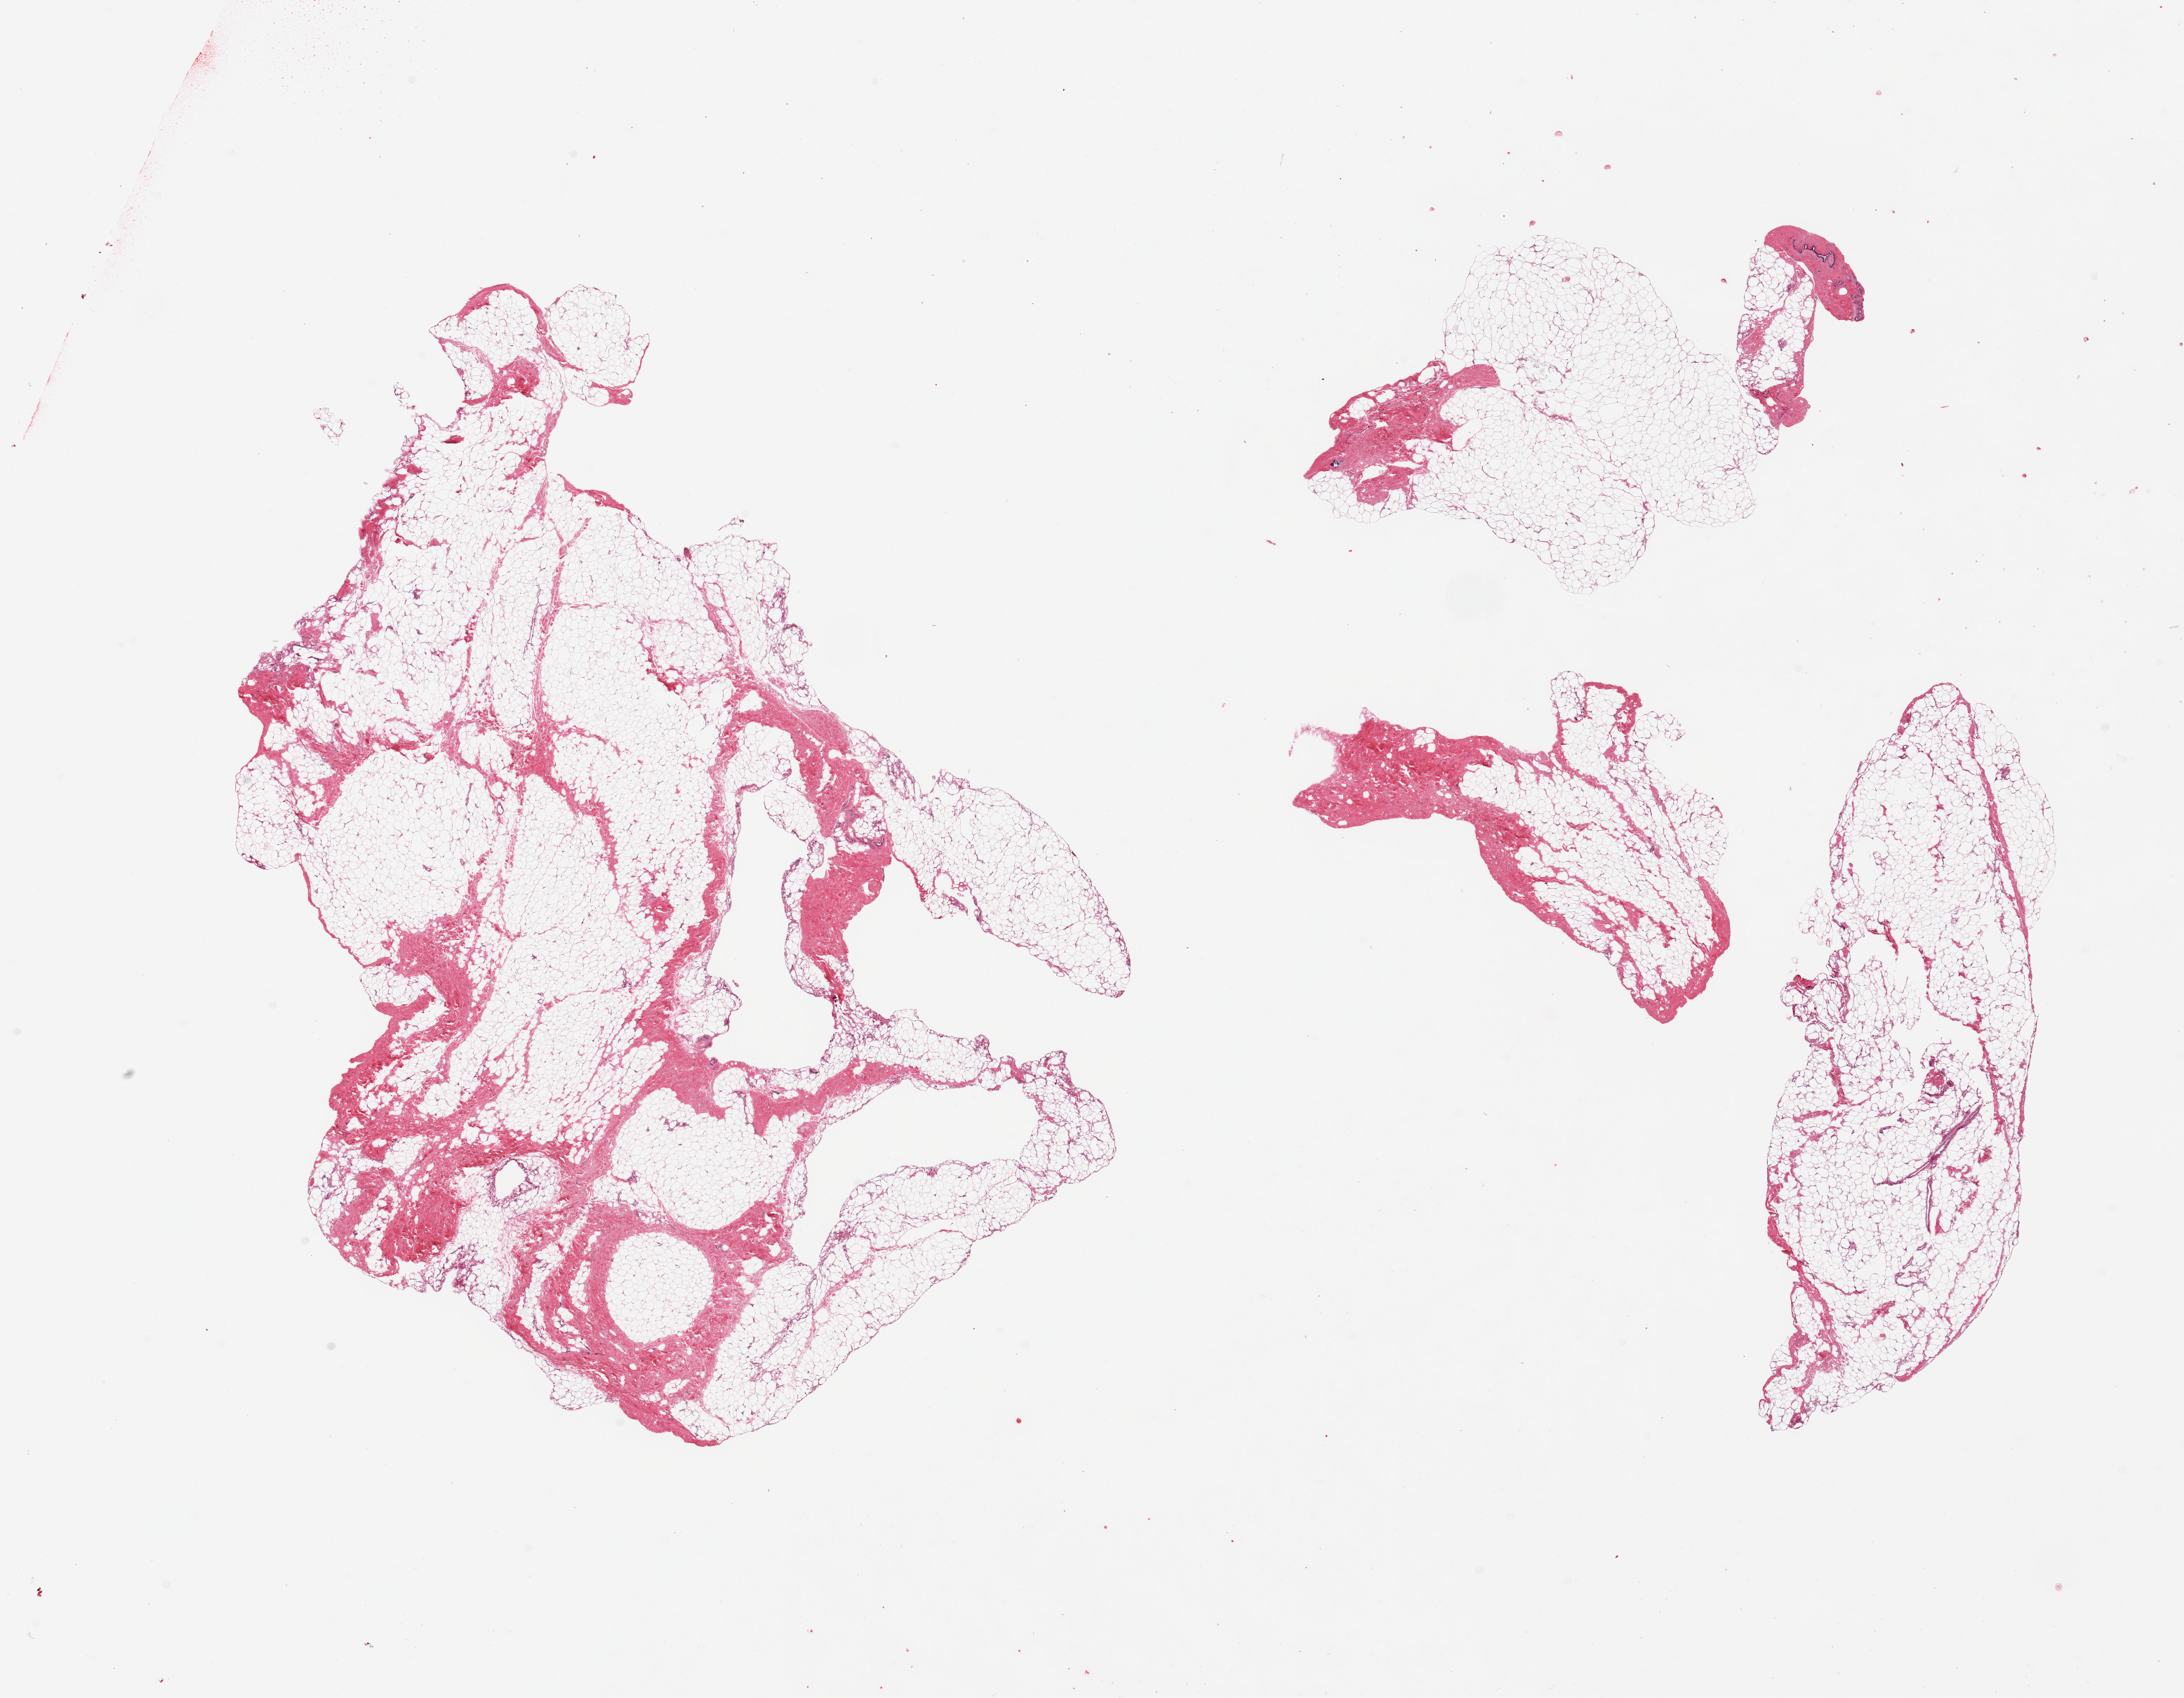
Whole-slide image, haematoxylin and eosin stain, brightfield — low-resolution overview of the scanned area, about 24.6 x 19.1 mm, PAXgene-fixed, paraffin-embedded tissue, sampled site (target tissue): breast, donor tissue sample. Donor: male.
- pathologist's review note for this sample: 2 pieces, fibroadipose elements only